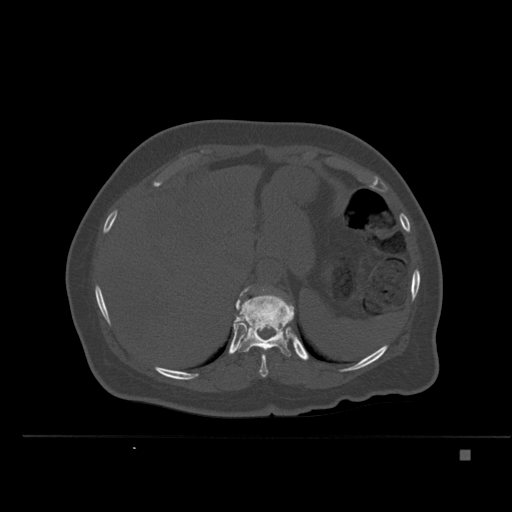
CT including the spine, one axial slice. Position 270 of 477 along the scan axis. Bone window (W 1800 / L 400 HU). 1.5 mm slice thickness. 512 × 512 image matrix, field of view 422 × 422 mm. Female patient, age 74 years. Case-level facts recorded for this patient, not image findings: primary cancer: colon.
Structures marked on this image (semi-automatic segmentation, software-assisted and operator-edited):
- T10 vertebra: bounding box [x1, y1, x2, y2] px = [247, 349, 269, 377]
- T11 vertebra: [236, 288, 295, 357]
- T12 vertebra: [247, 286, 266, 295]